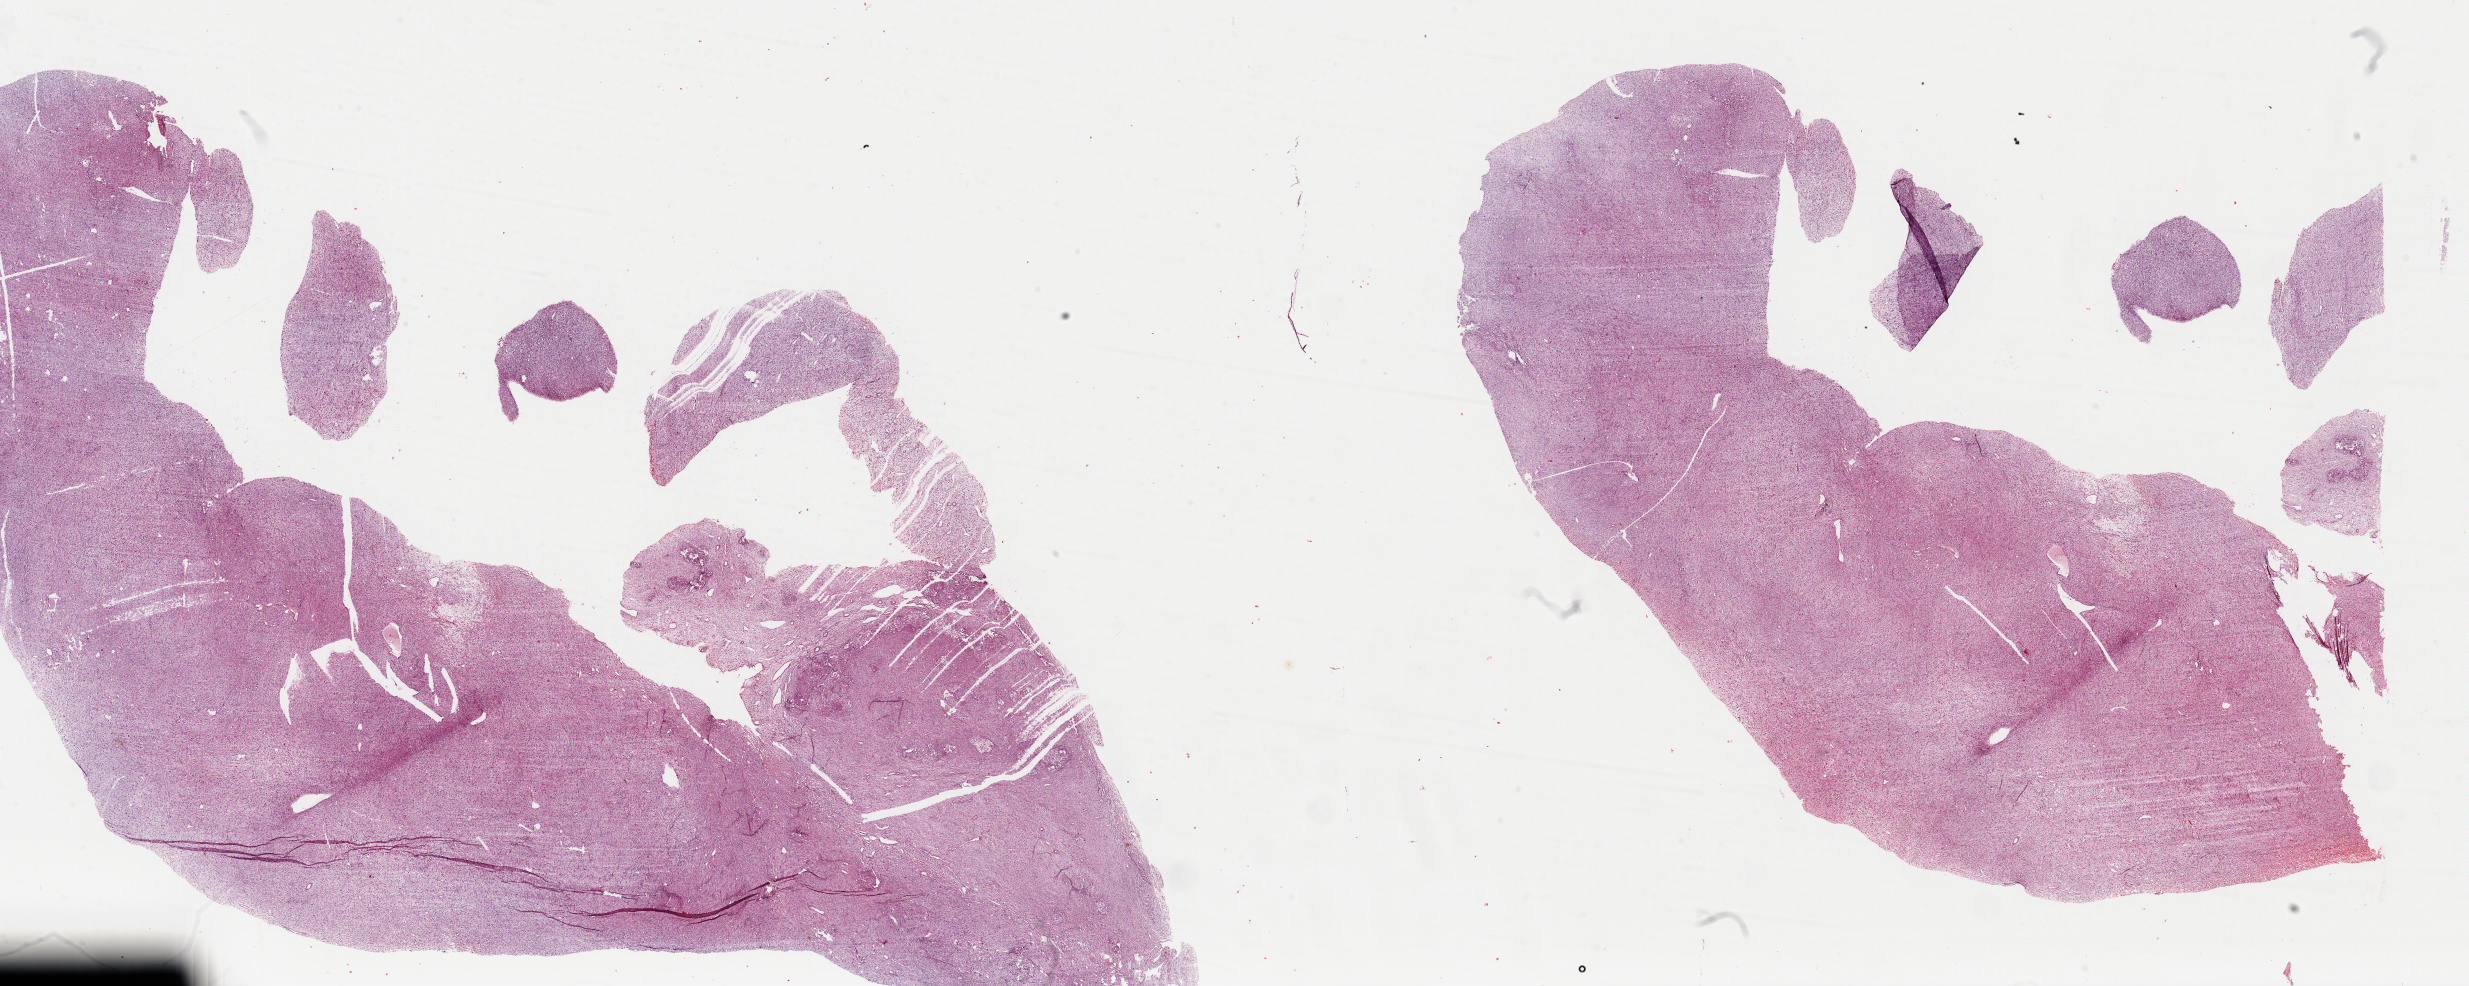
H&E-stained whole-slide image, a low-resolution overview of the entire scanned area, about 39.0 x 15.6 mm (acquisition: 40x scan), formalin-fixed paraffin-embedded (FFPE) diagnostic section, uterus, primary tumour sample. Female, age 55 years at initial diagnosis.
* histologic diagnosis: Mullerian mixed tumor (endometrium)
* FIGO stage: IB